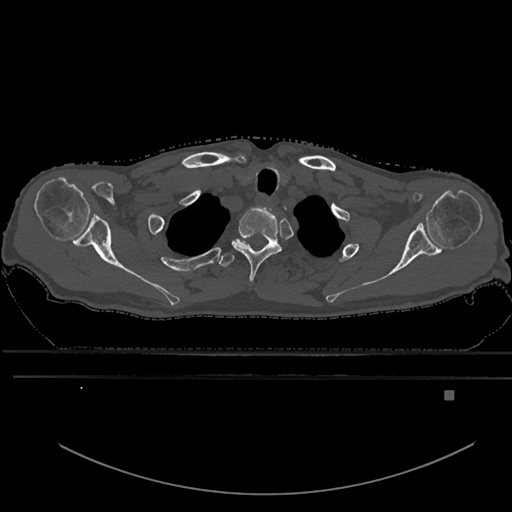
CT including the spine, one axial slice. Position 529 of 969 along the scan axis. Bone window (W 1800 / L 400 HU). 0.5 mm slice thickness. 512 × 512 image matrix, field of view 456 × 456 mm. Patient: male, 82 years. Case-level facts recorded for this patient, not image findings: primary cancer: prostate.
Outlined on this slice (semi-automatically segmented with operator editing):
- T1 vertebra: bounding box (x1, y1, x2, y2) in pixels: (232, 207, 282, 282)
- T2 vertebra: (219, 239, 280, 267)